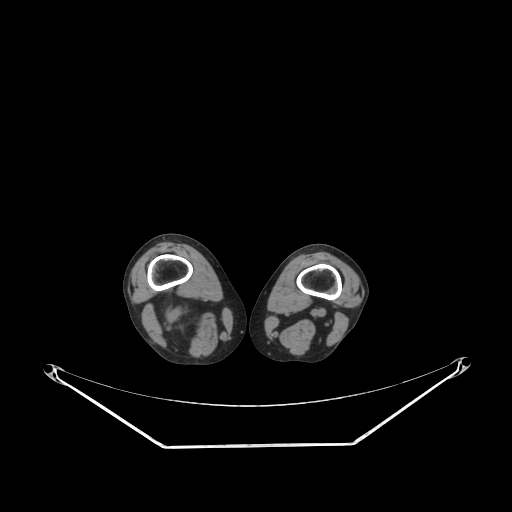
CT of an extremity soft-tissue mass (from a PET/CT study), one axial slice; slice 187 of 267 in the series (ordered by position); reconstruction kernel SOFT; 140 kVp; soft-tissue window (W 400 / L 40 HU); 3.75 mm slice thickness; 512 × 512 image matrix, field of view 500 × 500 mm. Female patient. Case-level facts recorded for this patient, not image findings: histological type: liposarcoma; site of the primary tumour: right thigh.
Structures marked on this image (expert contour drawn on MRI and transferred to this co-registered scan by the dataset authors):
- gross tumour volume (mass): bounding box (x1, y1, x2, y2) in pixels: (178, 311, 204, 325)